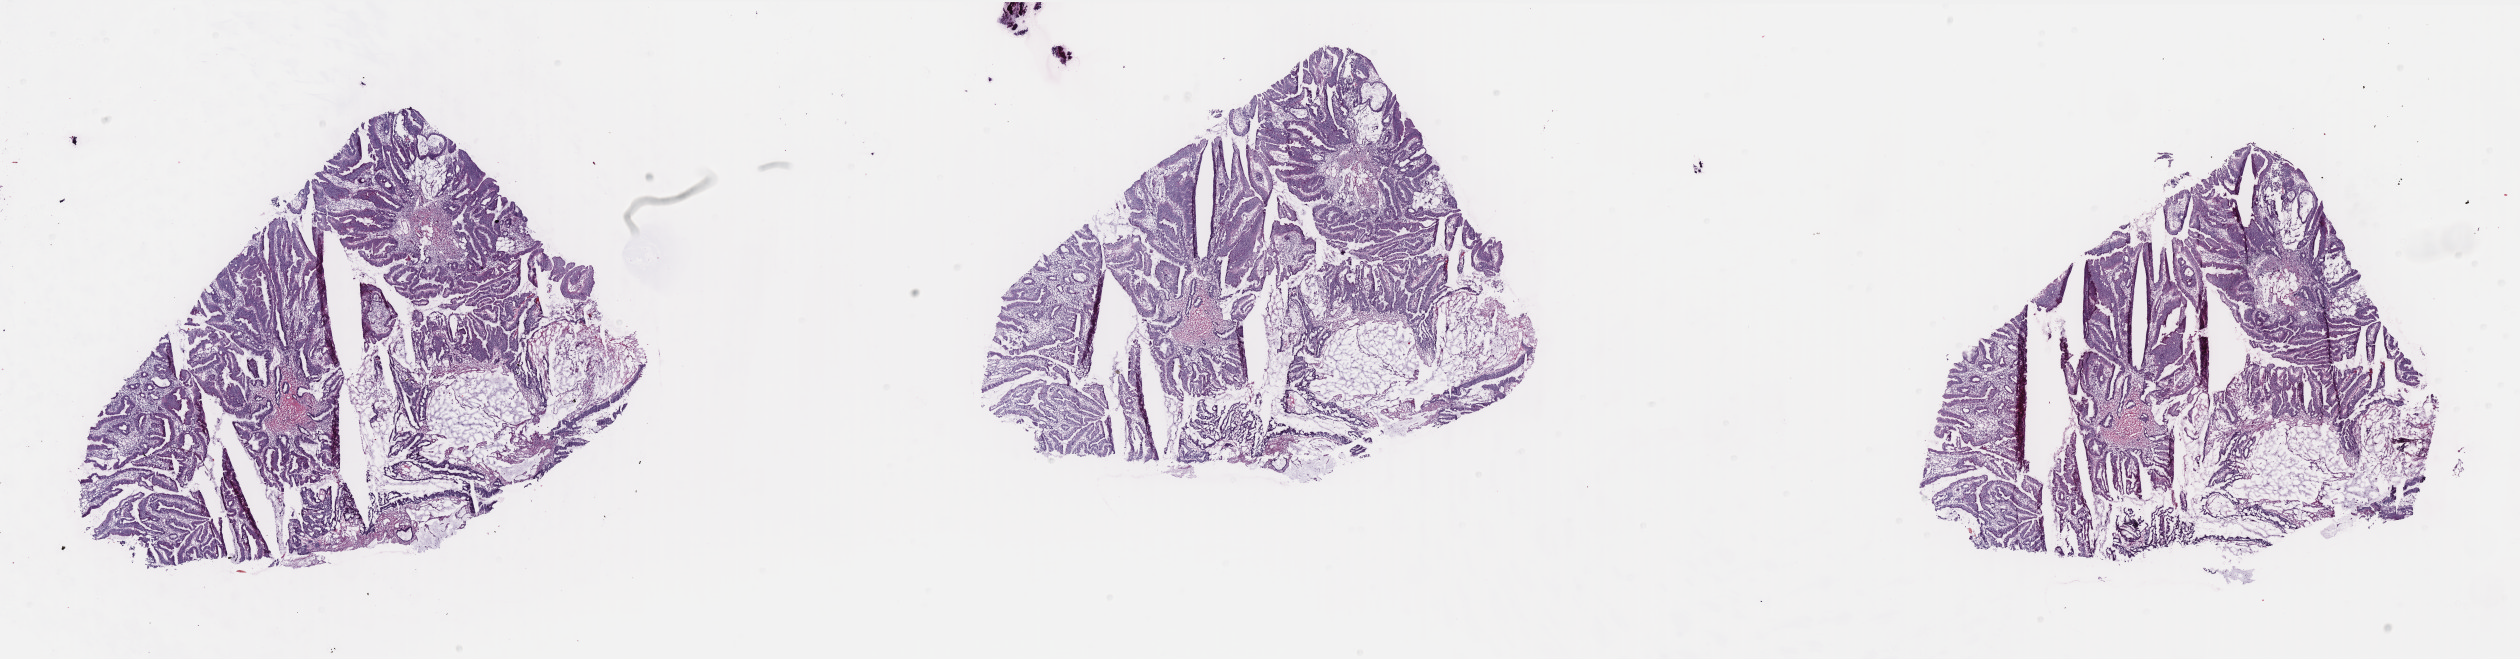
Whole-slide histology image, H&E-stained, shown as a low-resolution overview of the whole scanned area (about 40.4 x 10.6 mm, from a 40x scan). Frozen section. Colon, primary tumour sample. Male, age 81 years at initial diagnosis. Slide review estimates, as recorded: tumour cells 70%, tumour nuclei 70%, normal cells 0%, stromal cells 28%, necrosis 2%. Inflammatory infiltration, as recorded: lymphocyte infiltration 15%, monocyte infiltration 0%, neutrophil infiltration 3%.
AJCC pathologic stage: II (5th edition). Histologic diagnosis: Adenocarcinoma, NOS (descending colon). TNM: T3 N0 M0.